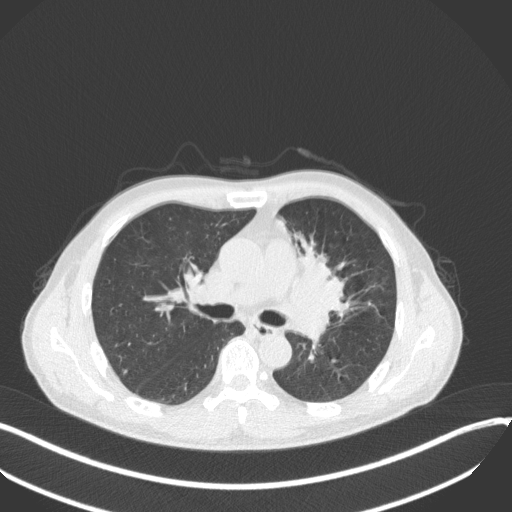
Chest CT, one axial slice. Position 203 of 411 along the scan axis. 120 kVp. Lung window (W 1500 / L -600 HU). 1 mm slice thickness. 512 × 512 image matrix, field of view 400 × 400 mm. Patient: male, 56 years. From the clinical record (not read from this slice): clinical TNM (as recorded): T2a N0 M0.
Structures marked on this image (bounding box drawn by a radiologist):
- lung tumour (recorded histology: squamous cell carcinoma): bounding box [x1, y1, x2, y2] px = [286, 228, 354, 328]